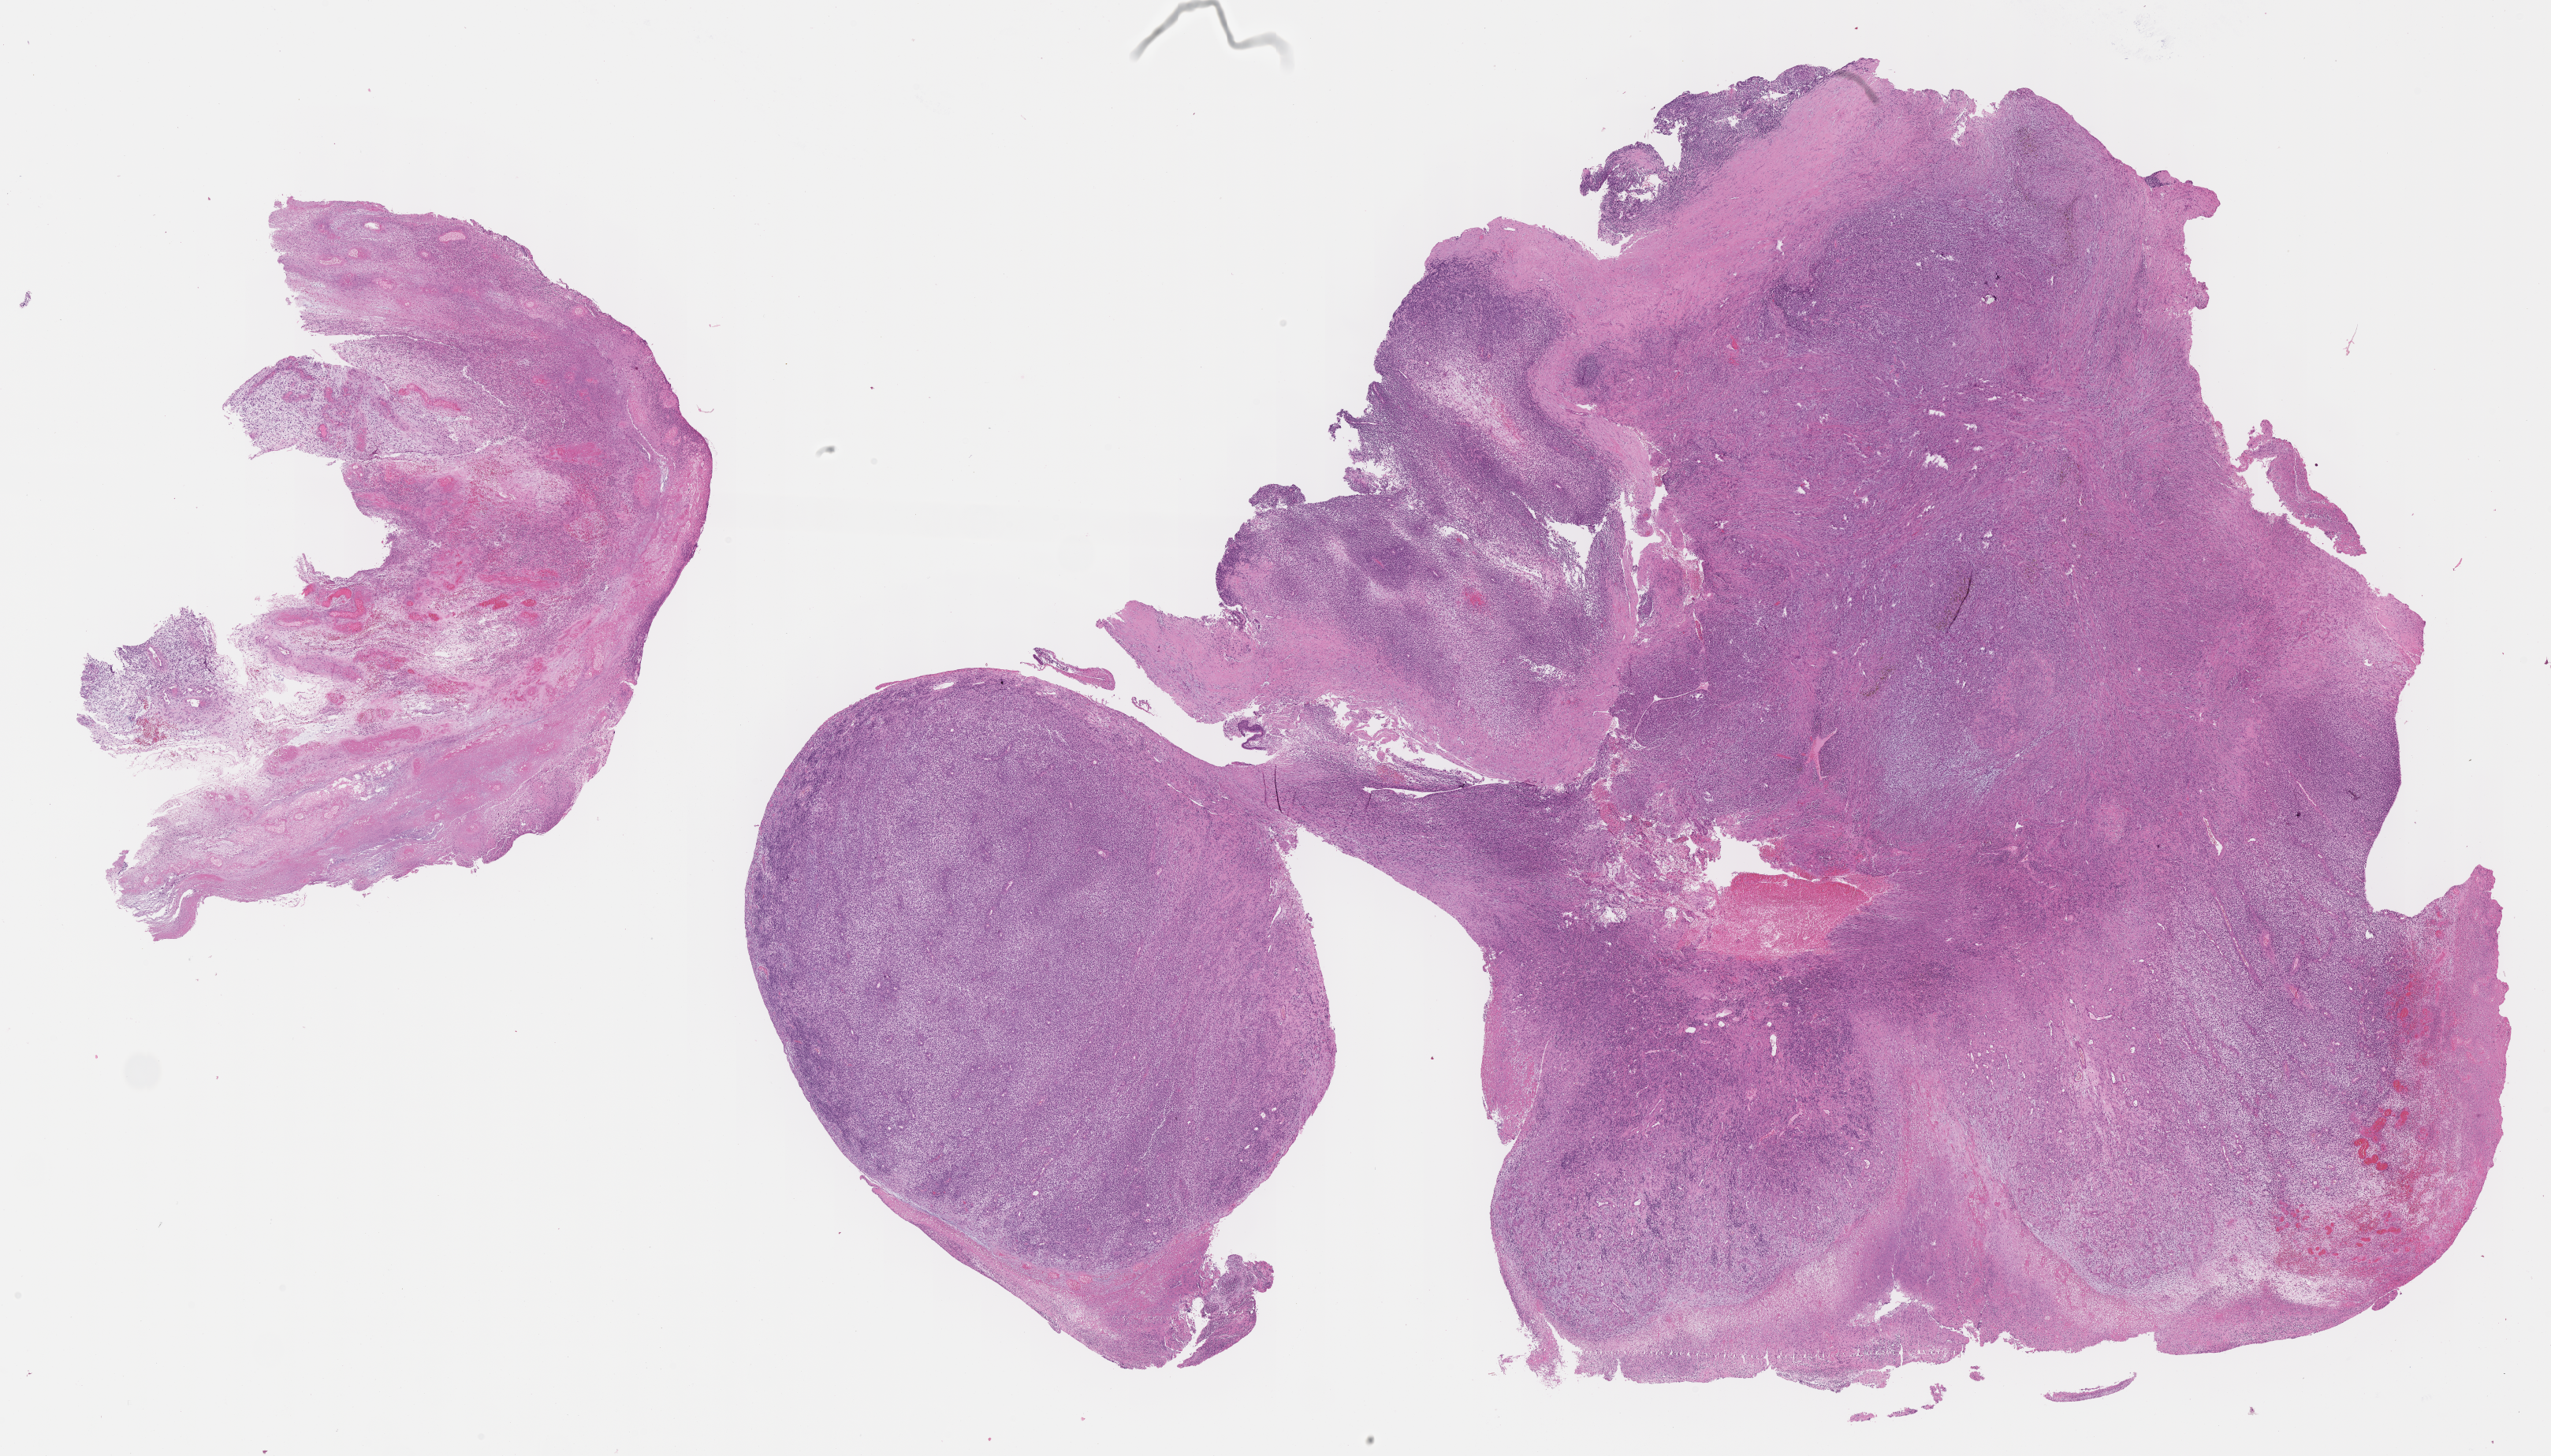
H&E whole-slide image of tumor tissue, low-resolution overview of the scanned area, about 26.2 x 14.9 mm, formalin-fixed paraffin-embedded section, site: nasopharyngeal. Male patient, age at diagnosis 2.8 years.
• diagnosis: rhabdomyosarcoma; histological classification: embryonal rhabdomyosarcoma
• stage (as recorded): 4